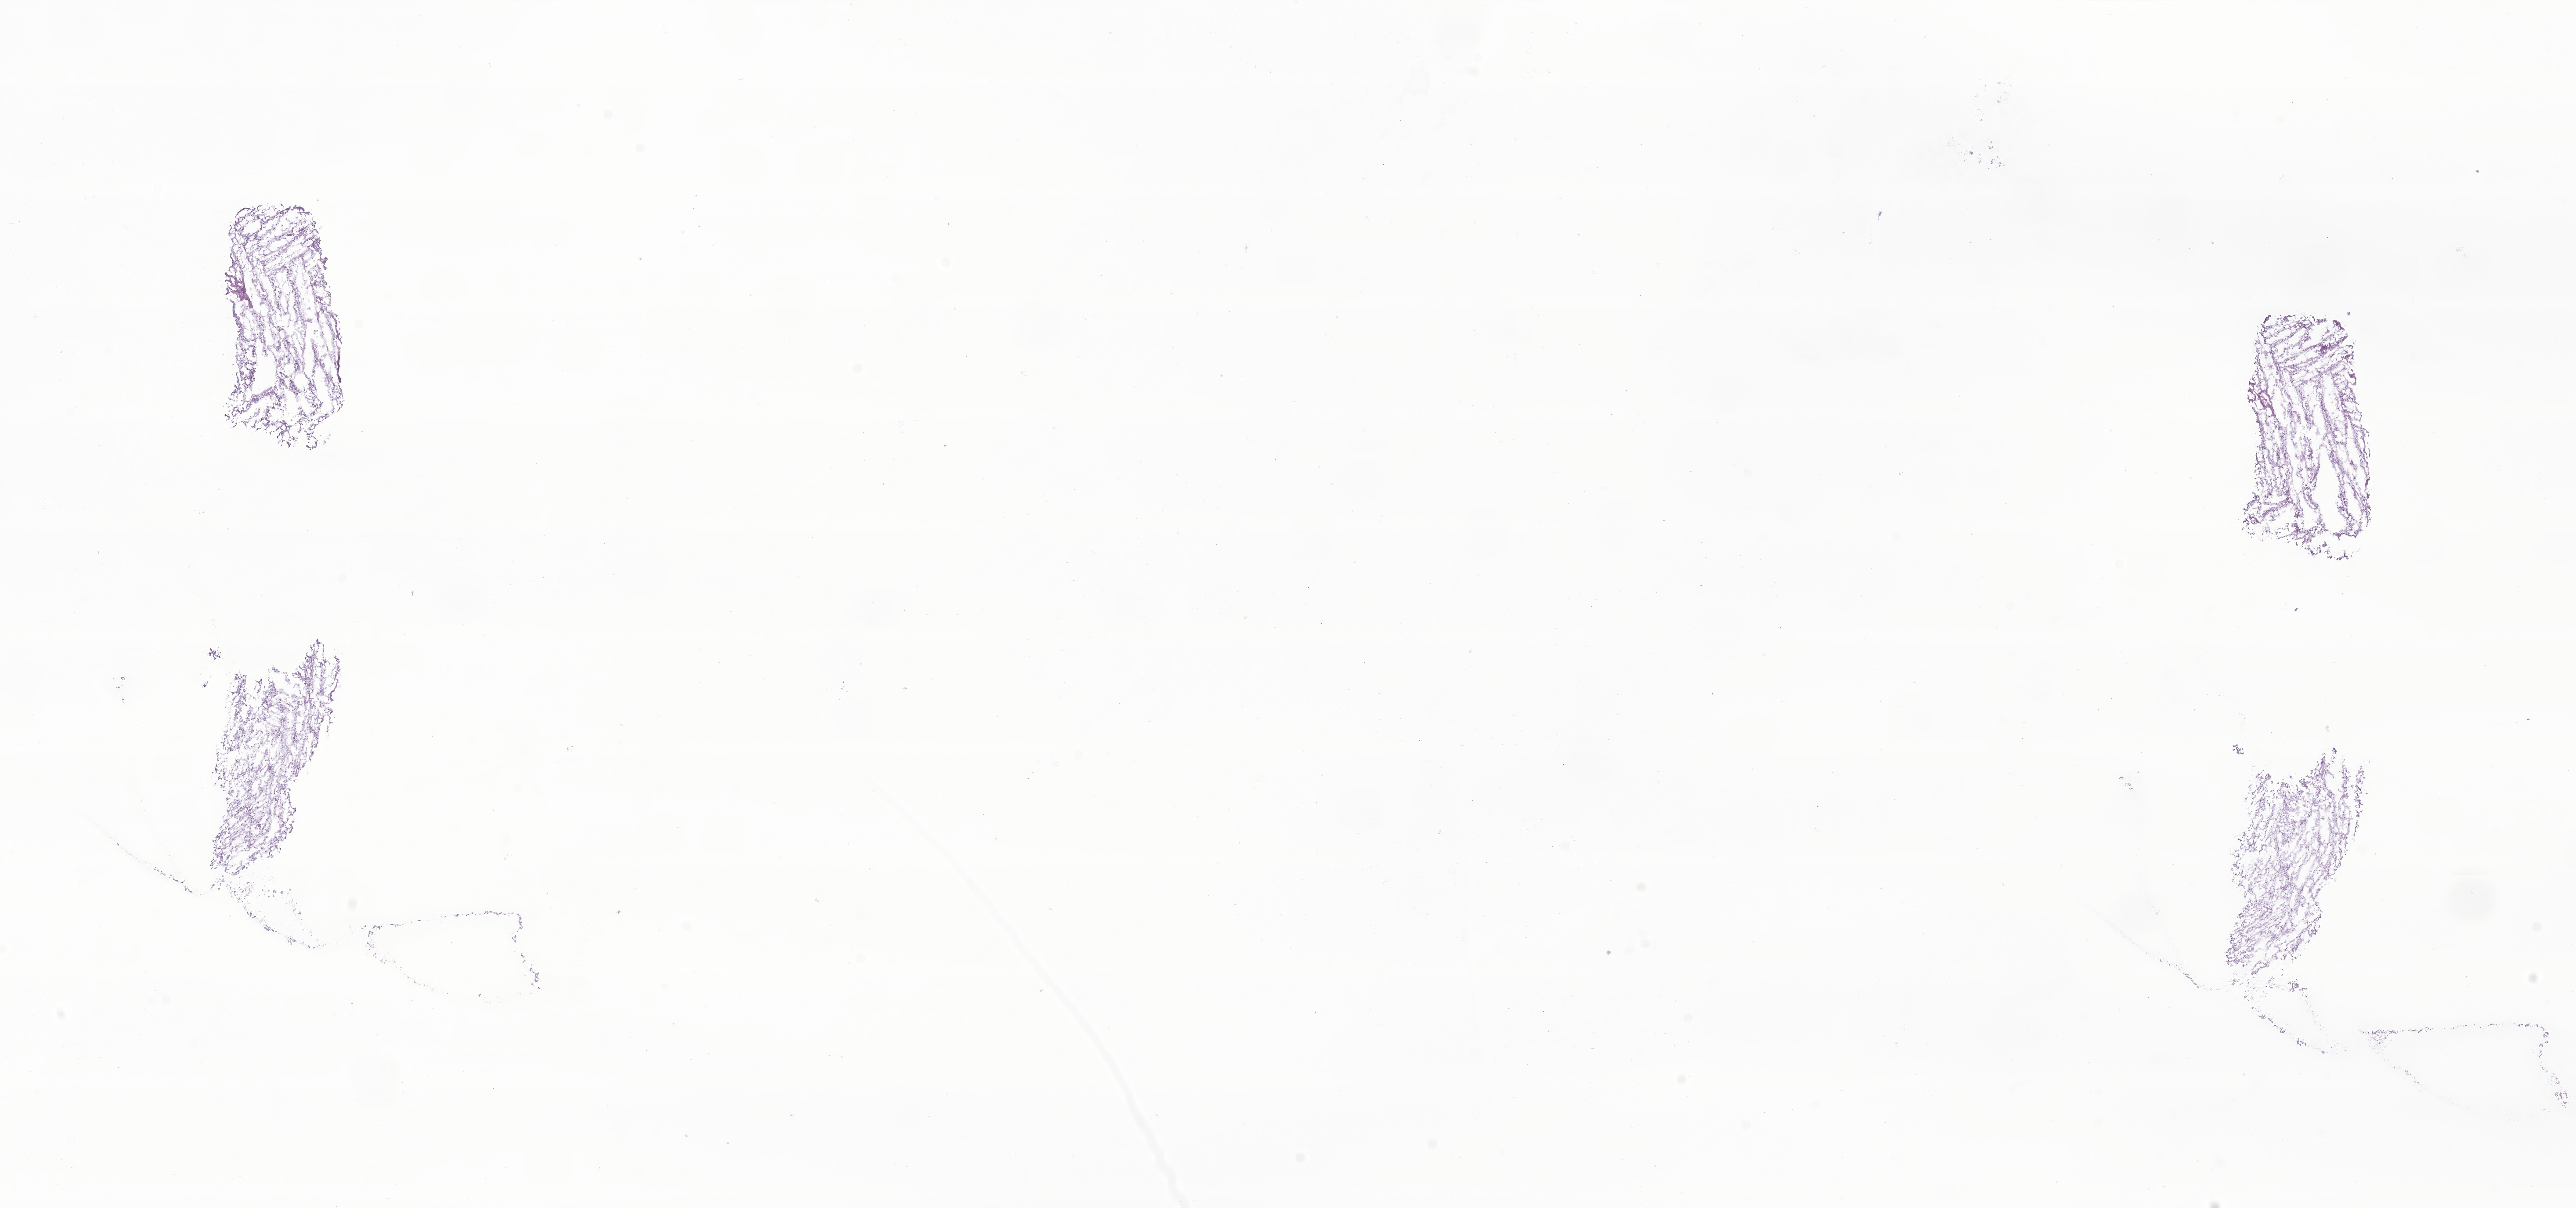
Hematoxylin and eosin (H&E) whole-slide image of tumor tissue from the brain — whole scanned area (about 24.7 x 11.6 mm) shown as a low-resolution overview. Cryosection (OCT / tissue freezing medium). Female patient, age 264 days.
Diagnosis (ICD-O-3 morphology term): Glioma, malignant.